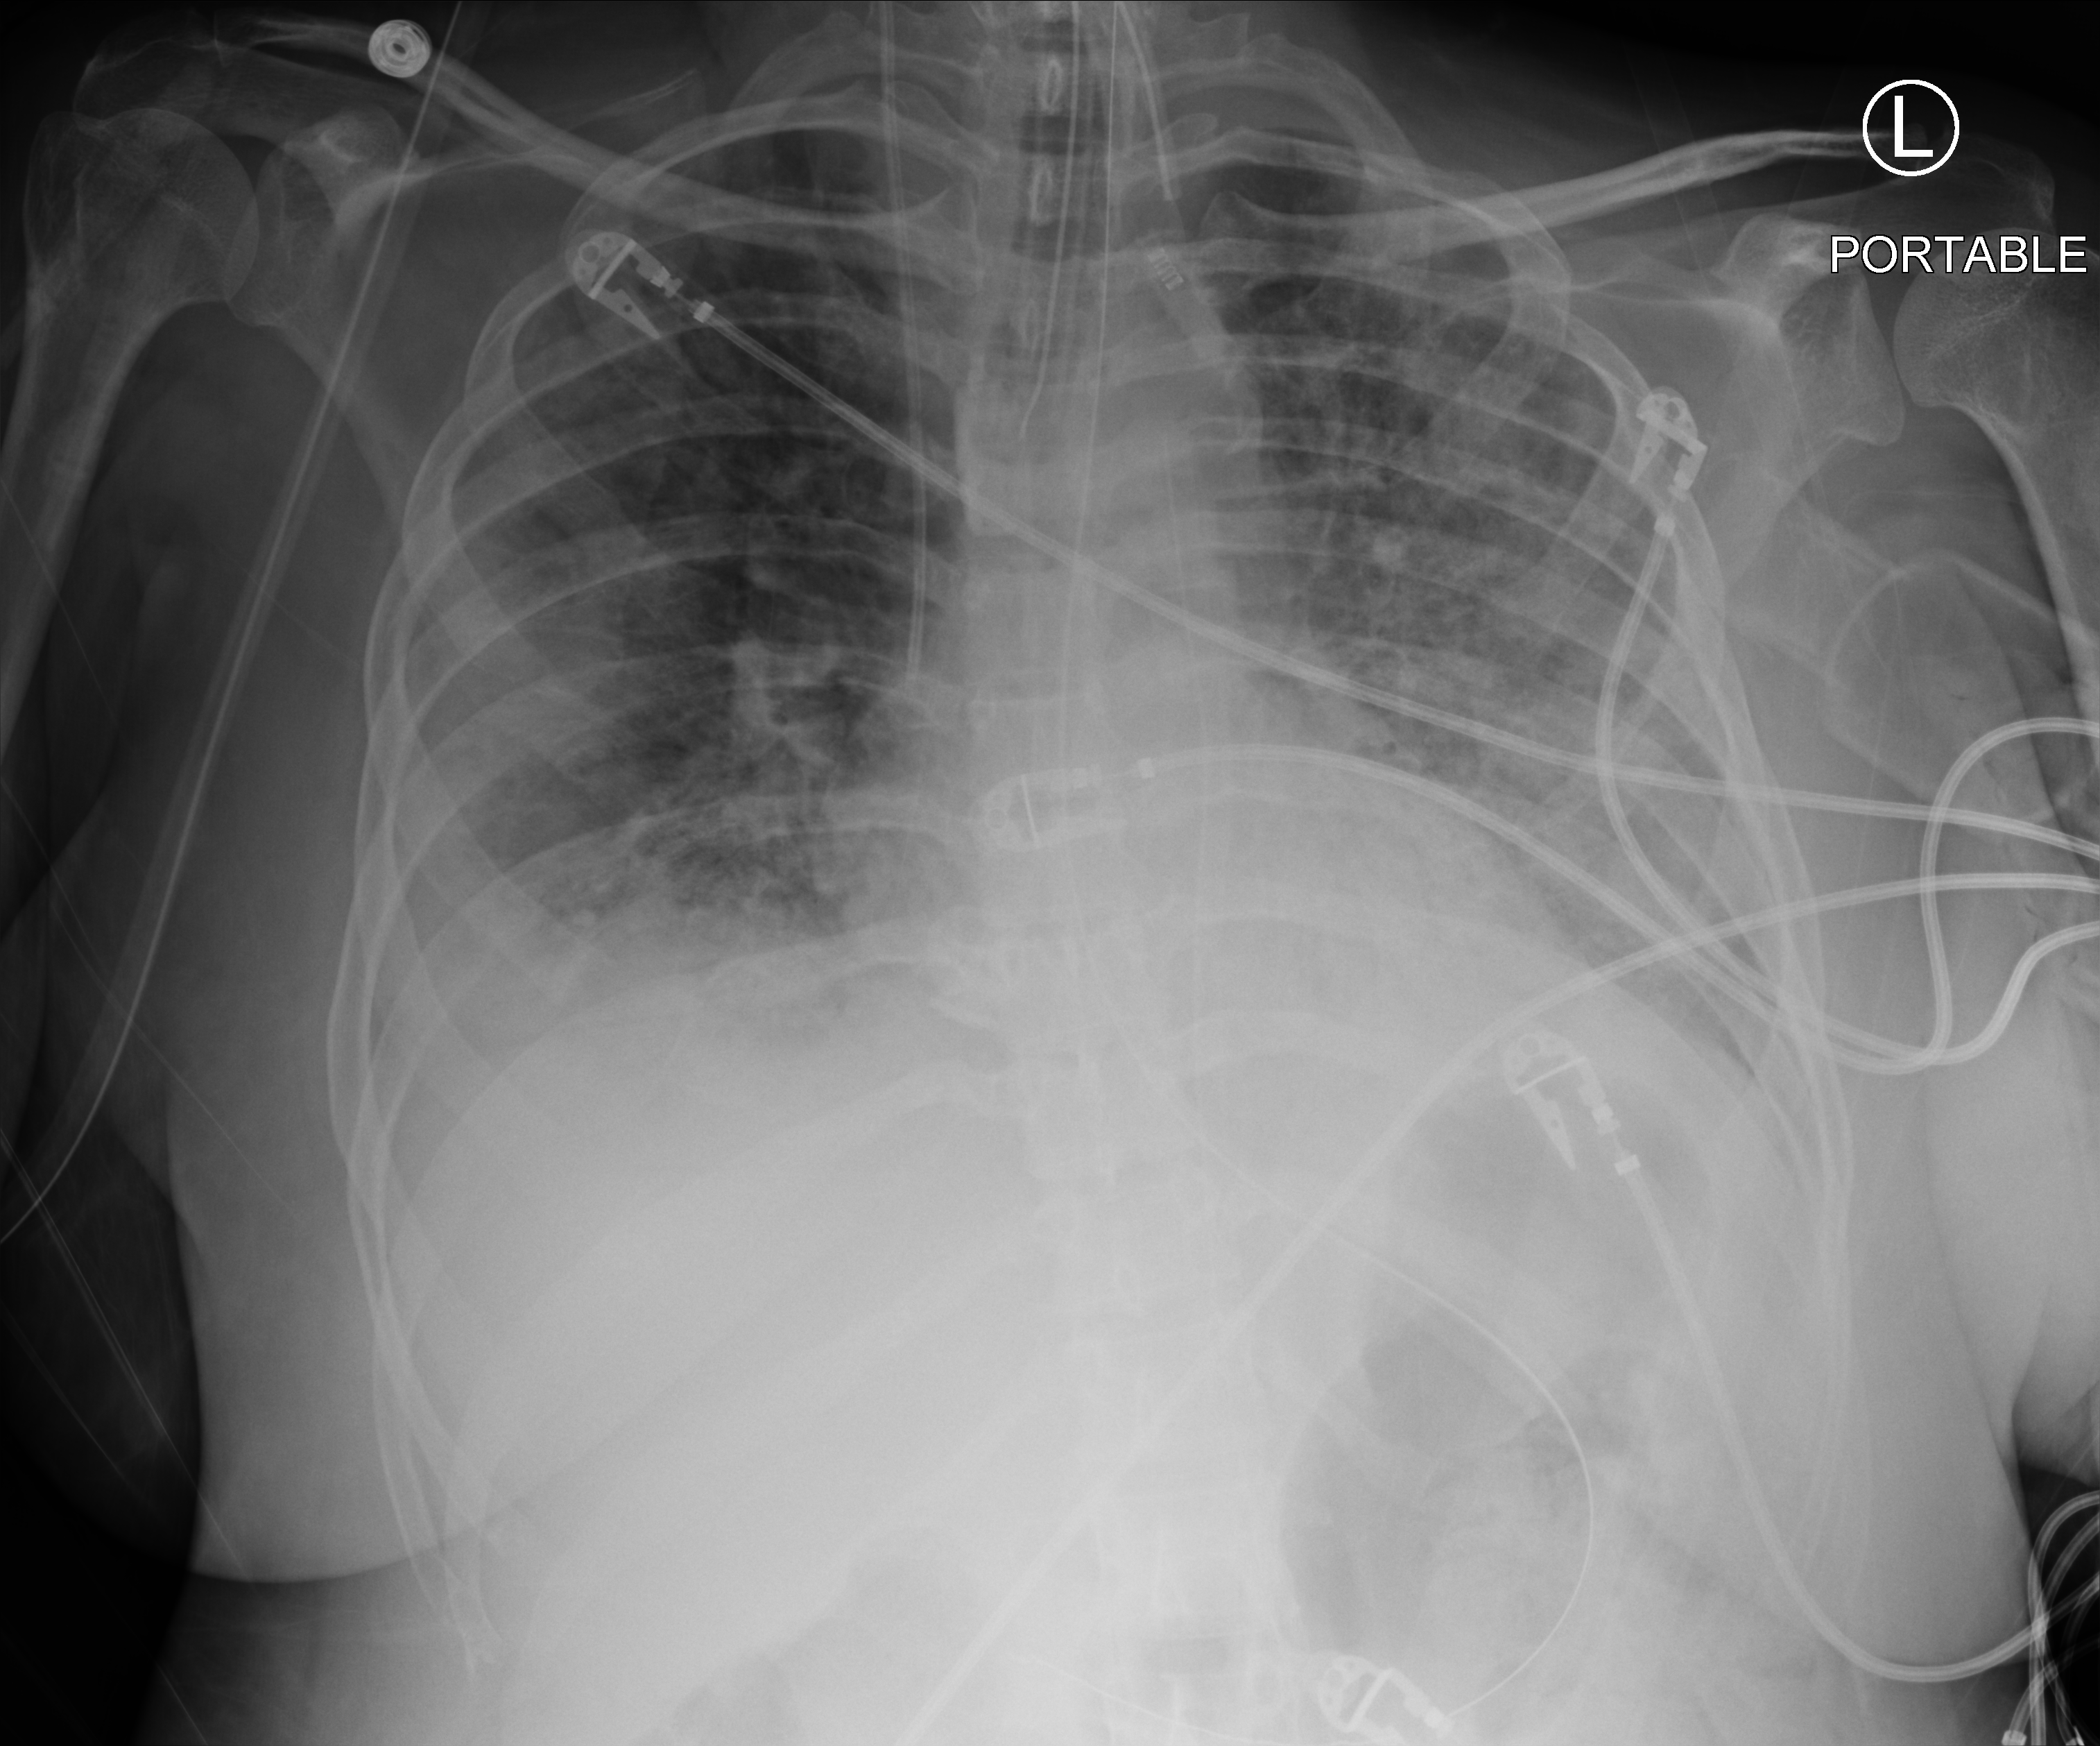
Bedside chest radiograph (computed radiography), anteroposterior (AP) projection. Patient hospitalised with COVID-19, aged 18–59 years.
Hospital-stay facts (about this admission, not read from this image; timing relative to this image not recorded):
- COPD (admission record): no